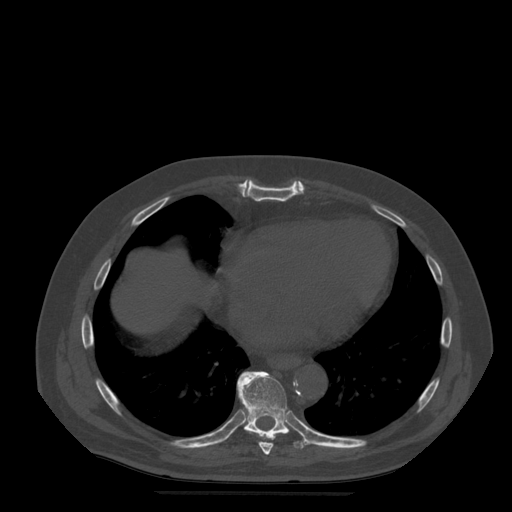
CT including the spine, one axial slice. Position 299 of 522 along the scan axis. Bone window (W 1800 / L 400 HU). 1.25 mm slice thickness. 512 × 512 image matrix, field of view 420 × 420 mm. Patient age 72 years. From the clinical record (not read from this slice): primary cancer: prostate.
Structures marked on this image (semi-automatic segmentation, software-assisted and operator-edited):
- T8 vertebra: bounding box <247,431,274,455> (left, top, right, bottom; pixels)
- T9 vertebra: <237,372,310,449>